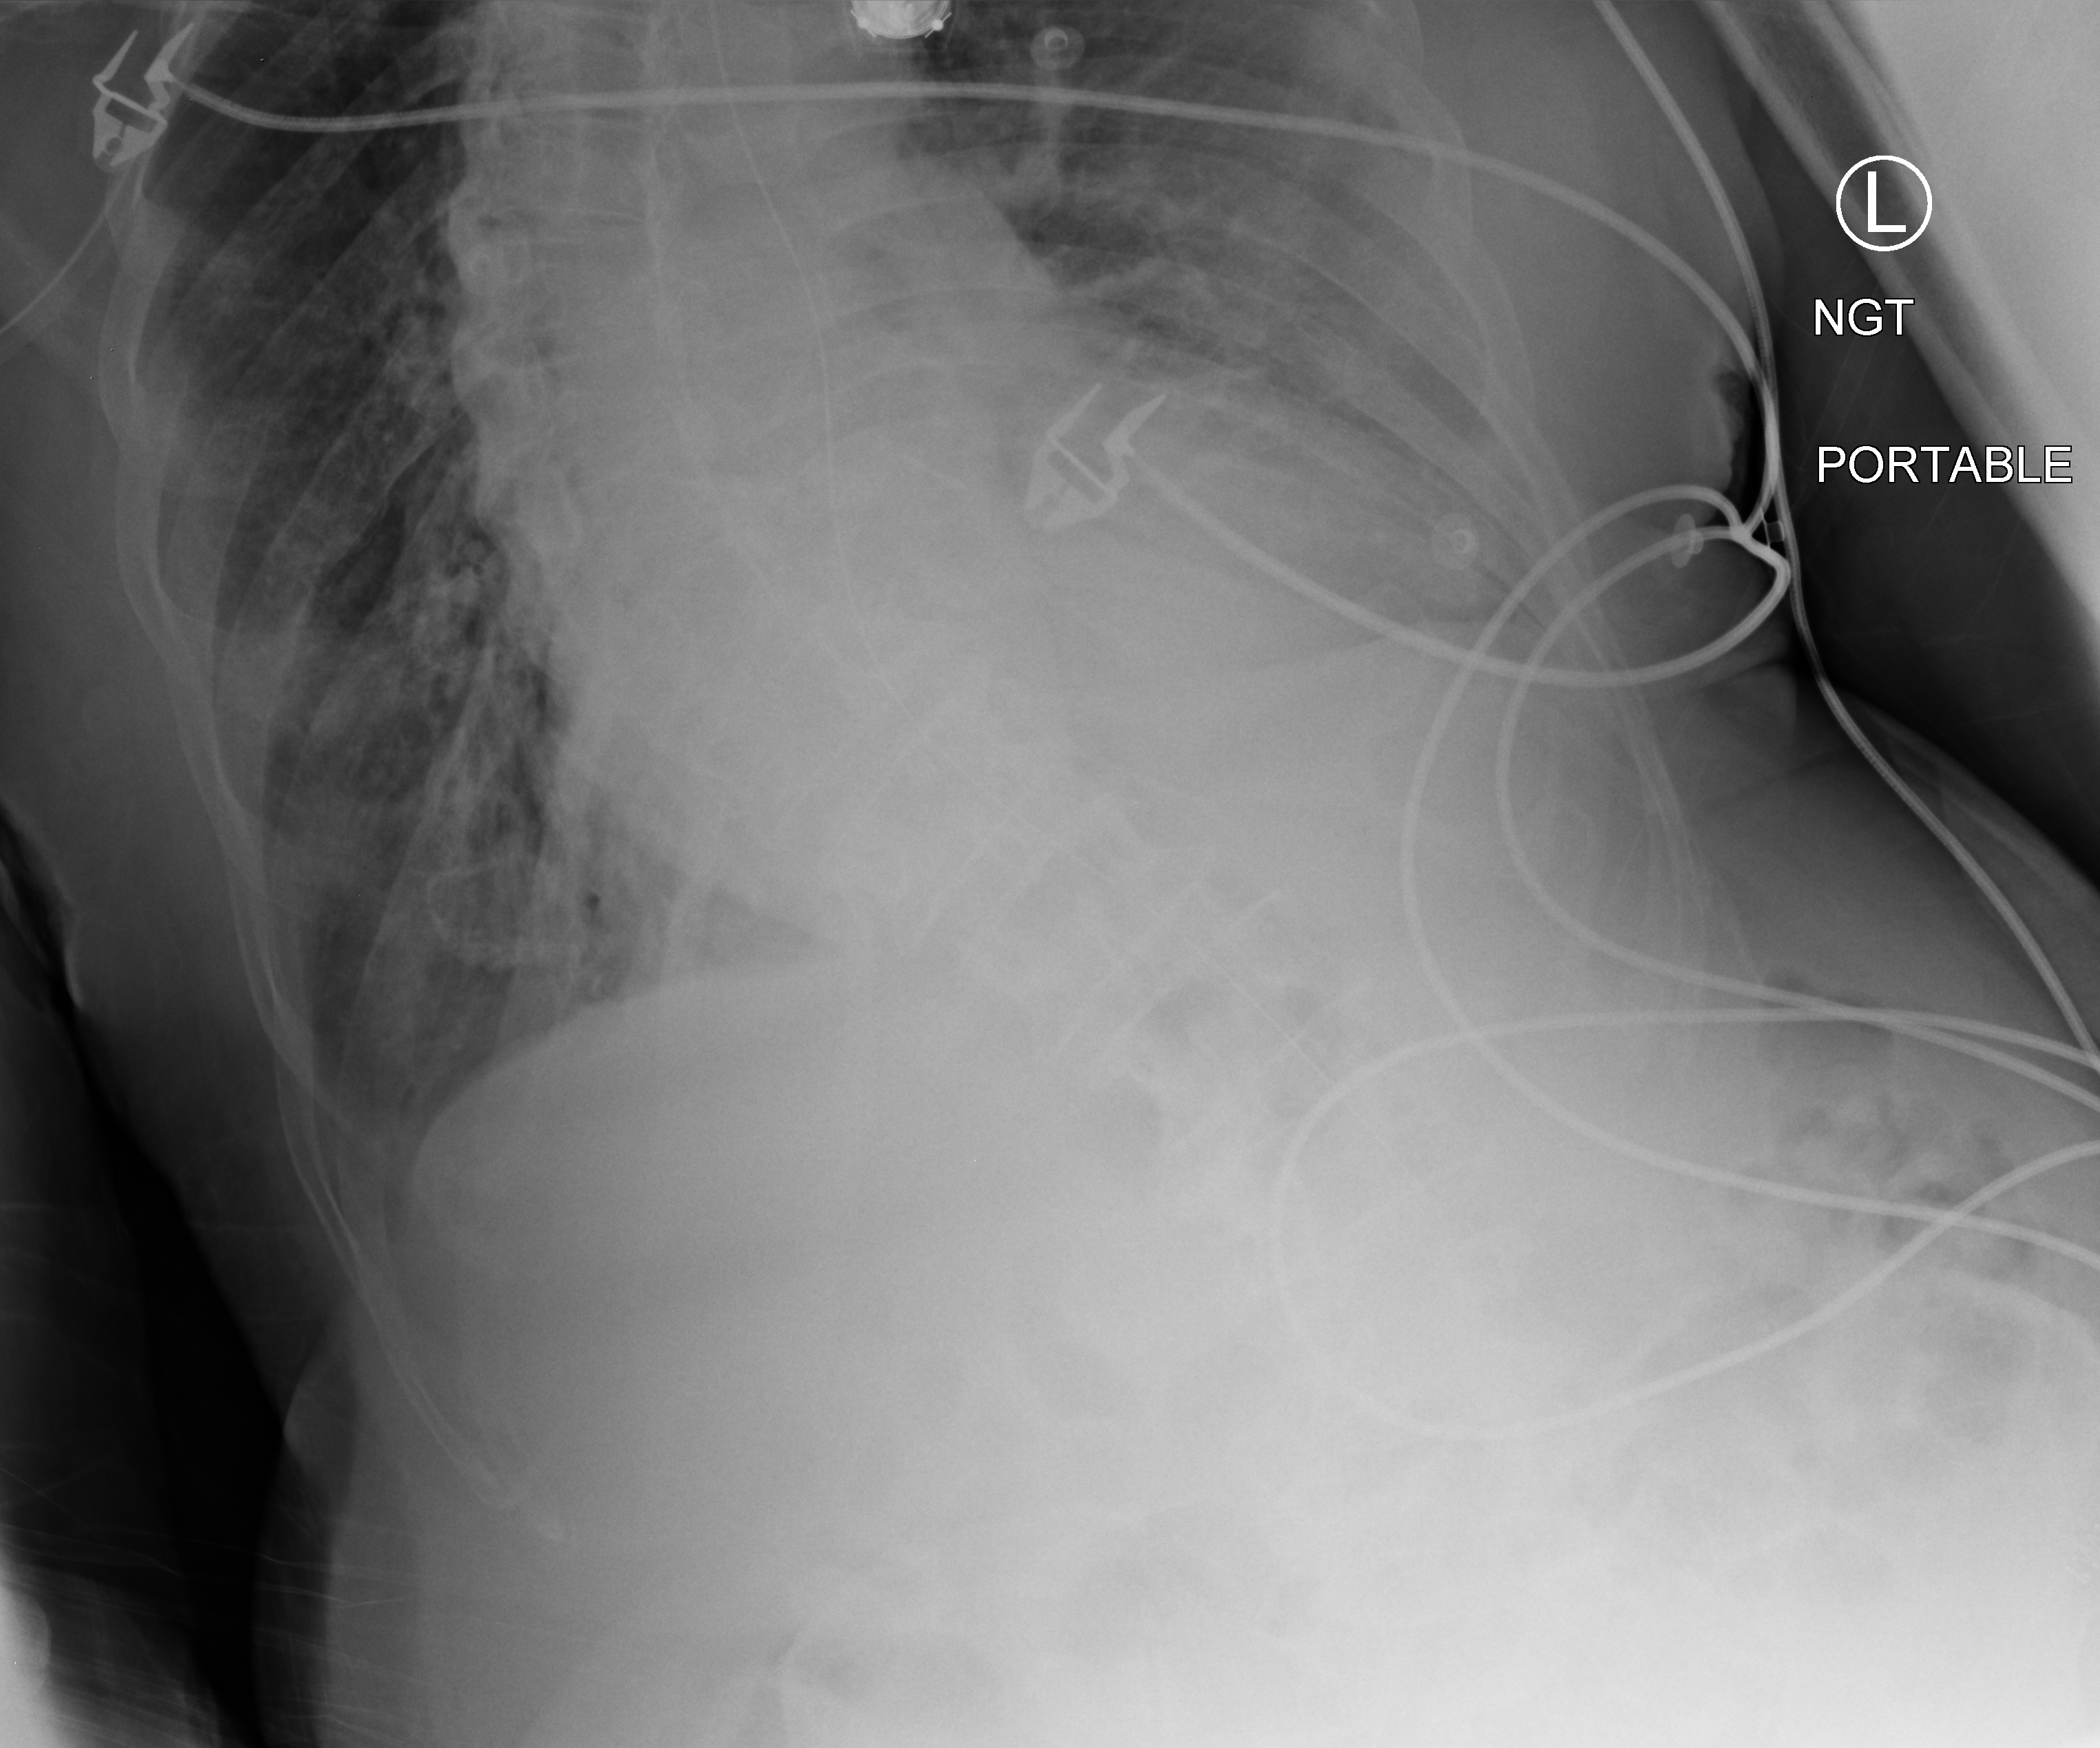
Portable chest radiograph, anteroposterior (AP) projection. Male patient hospitalised with COVID-19, age 75–90 years.
Hospital-stay facts (about this admission, not read from this image; timing relative to this image not recorded): admitted to intensive care during this hospital stay: no; mechanically ventilated during this hospital stay: no.